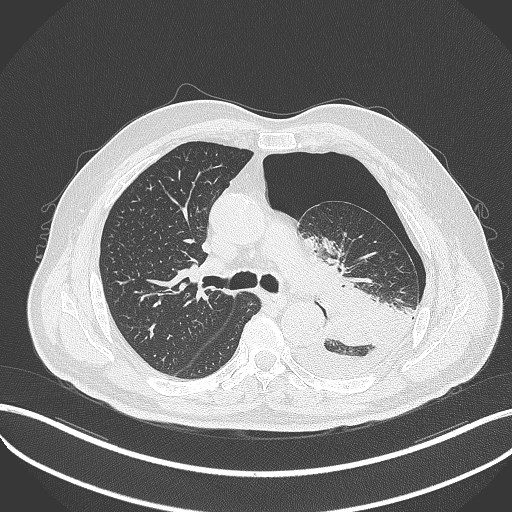
Chest CT, one axial slice. Position 330 of 464 along the scan axis. Lung window (W 1500 / L -600 HU). 512 × 512 image matrix, field of view 400 × 400 mm. Patient: male, 76 years. Case-level facts recorded for this patient, not image findings: clinical TNM (as recorded): T3 N0 M1b.
Annotated regions visible in this slice (rectangle marked by the reading radiologist):
- lung tumour (recorded histology: adenocarcinoma): bounding box <319,281,395,346> (left, top, right, bottom; pixels)